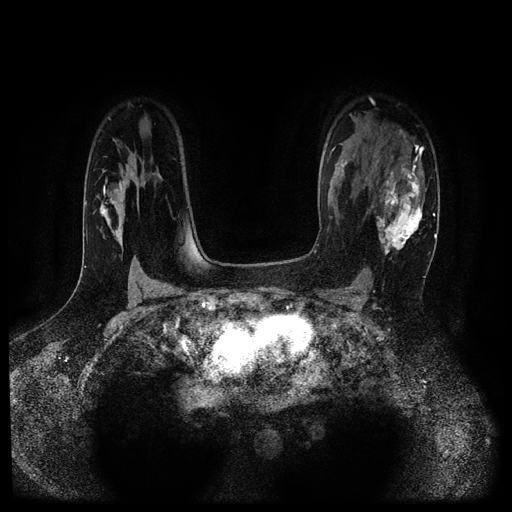
Breast MRI (dynamic contrast-enhanced, multi-phase), one axial slice; slice 72 of 116 in the series (ordered by position); dynamic contrast-enhanced series, time point 2 of 5 at this slice position (early post-contrast); 1.5 T; TE 2.7 ms, TR 5.4 ms; 512 × 512 image matrix, field of view 330 × 330 mm. Patient: female, 43 years.
Outlined on this slice (semi-automatically segmented with operator editing):
- breast lesion (labelled 'tumour' in the annotation; benign lesions carry a separate 'benign' label): bounding box (x1, y1, x2, y2) in pixels: (373, 164, 428, 260)